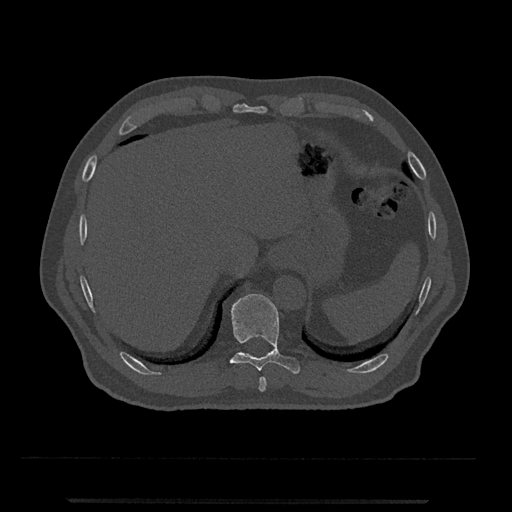
CT including the spine, one axial slice; slice 517 of 797 in the series (ordered by position); bone window (W 1800 / L 400 HU); 0.5 mm slice thickness; 512 × 512 image matrix, field of view 419 × 419 mm. Patient: male, 63 years. Case-level facts recorded for this patient, not image findings: primary cancer: prostate.
Annotated regions visible in this slice (semi-automatic segmentation, software-assisted and operator-edited):
- T10 vertebra: box from (x=230, y=293) to (x=301, y=374) px
- T9 vertebra: (x=259, y=377)–(x=267, y=392)